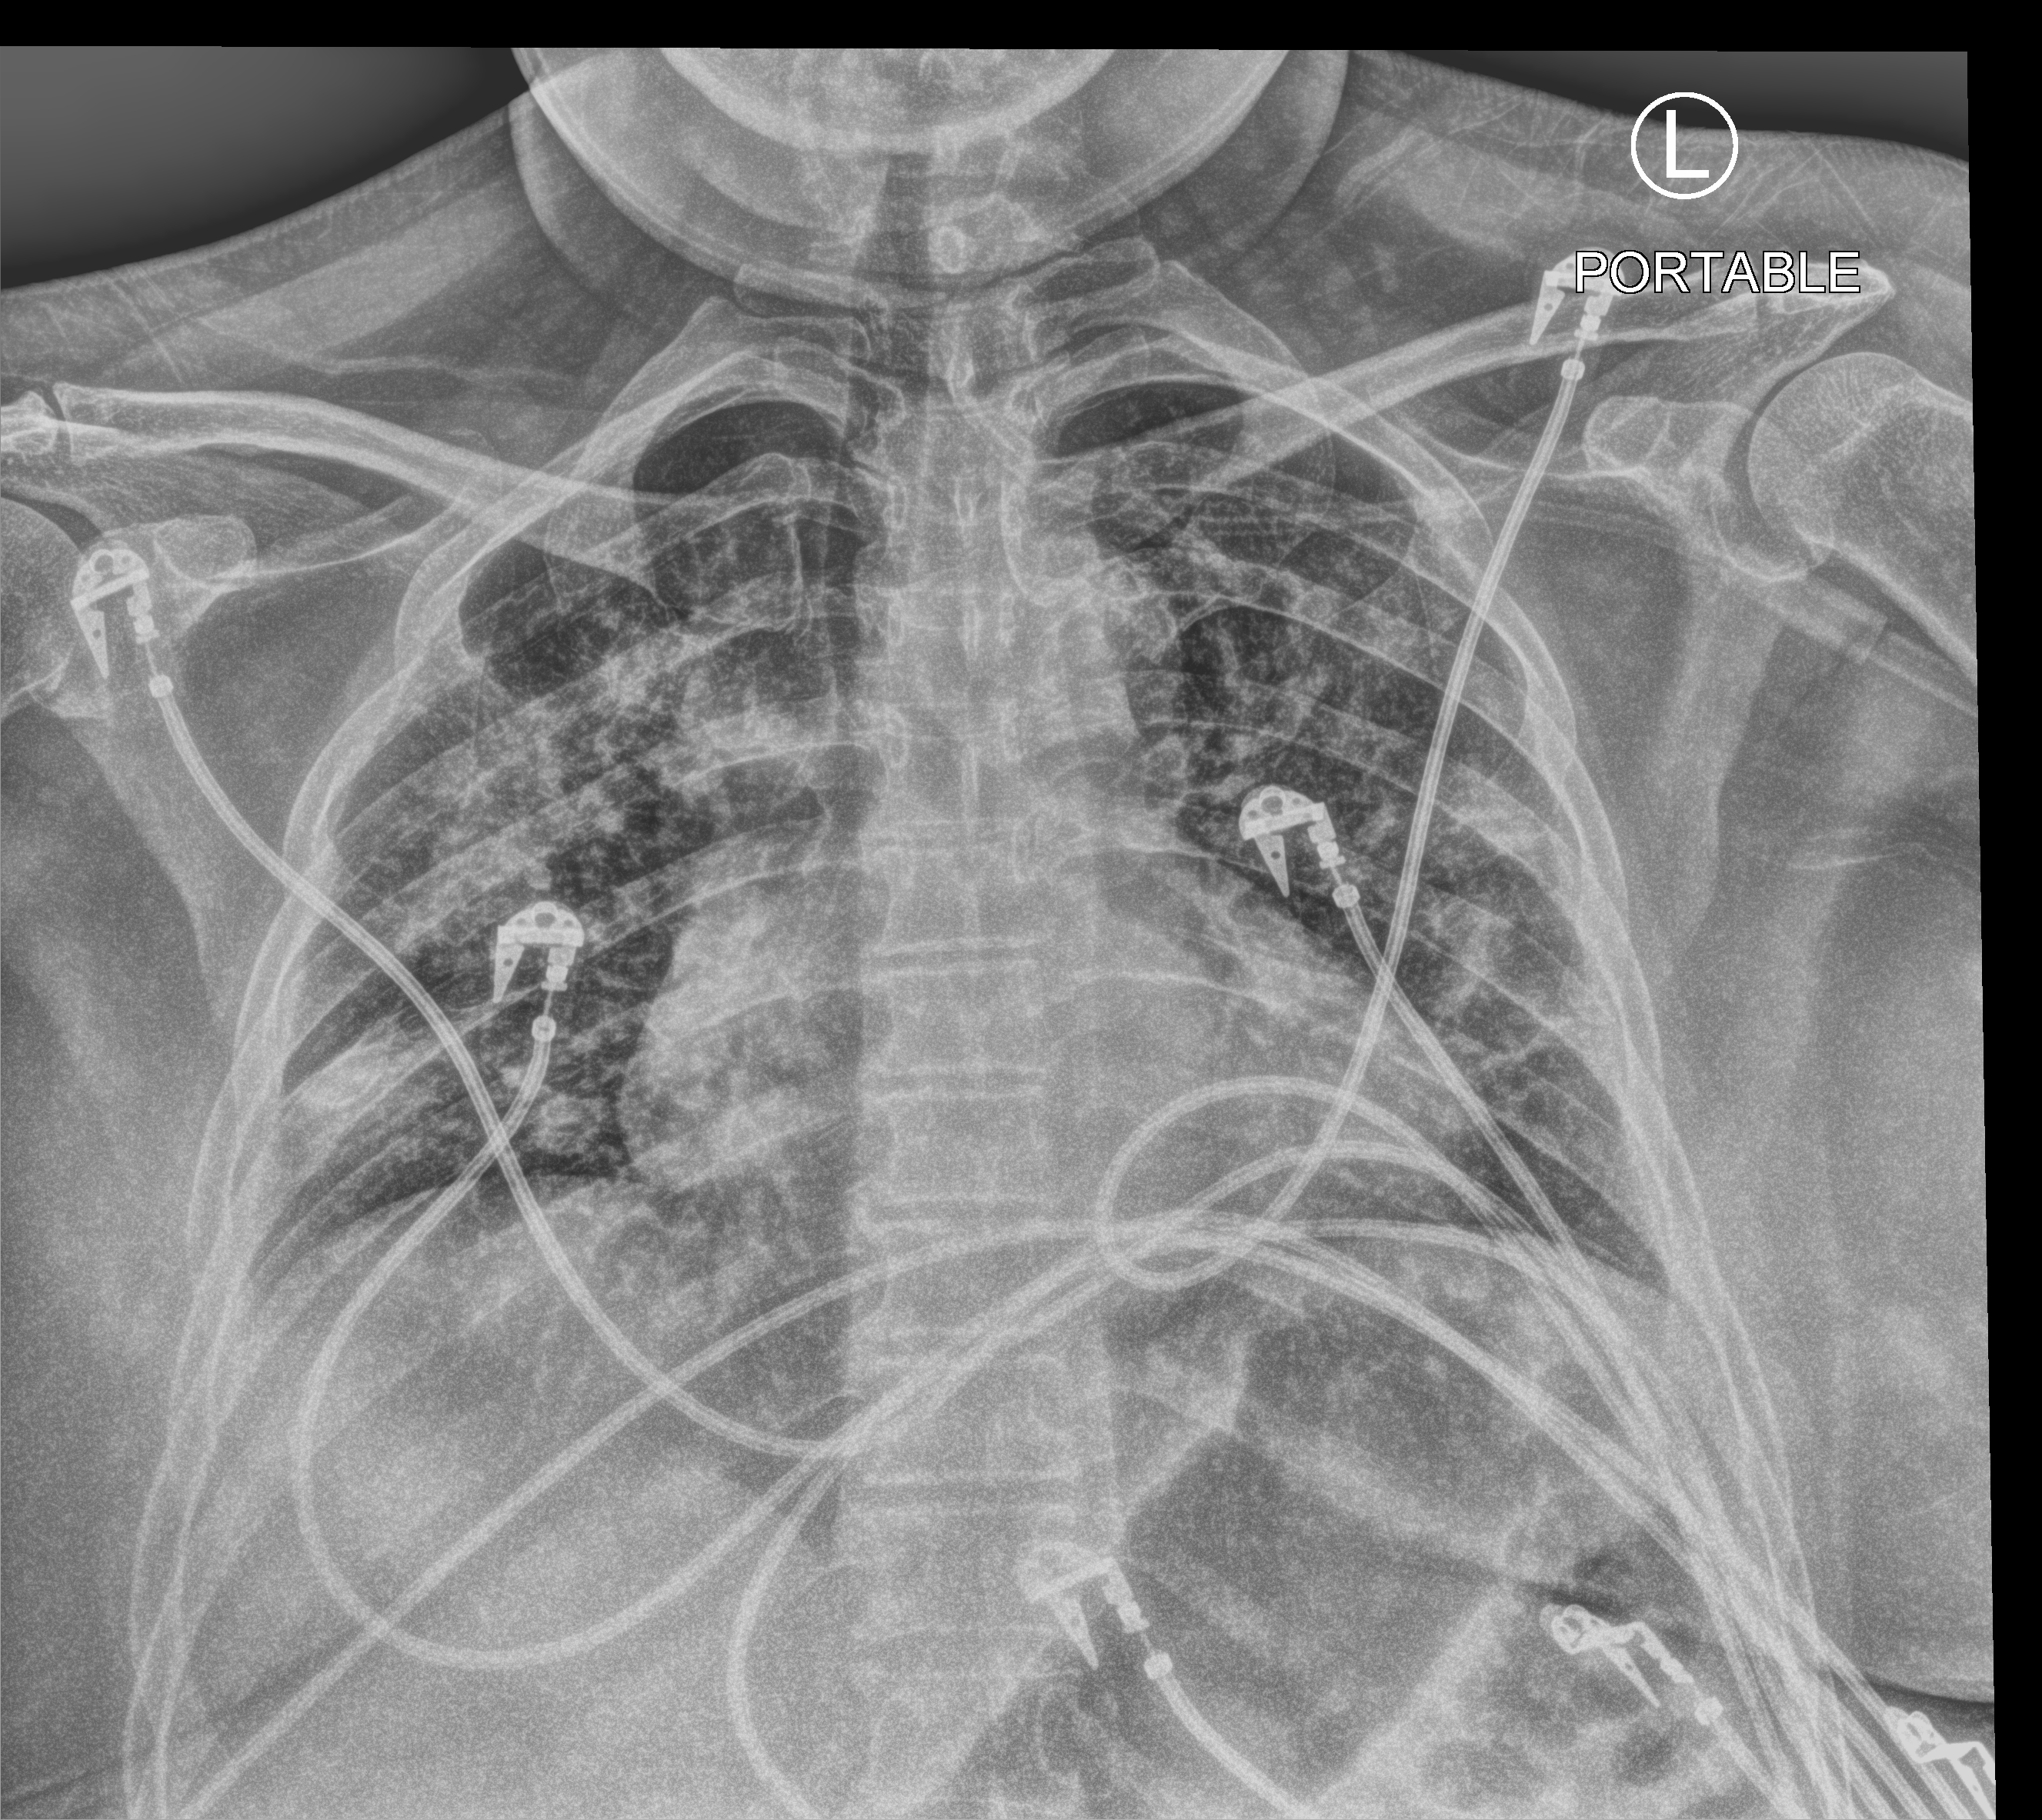
Portable chest radiograph, anteroposterior (AP) projection. Female patient hospitalised with COVID-19, age 18–59 years.
Hospital-stay facts (about this admission, not read from this image; timing relative to this image not recorded):
- mechanically ventilated during this hospital stay: no
- smoking status (admission record): never
- diabetes (admission record): no